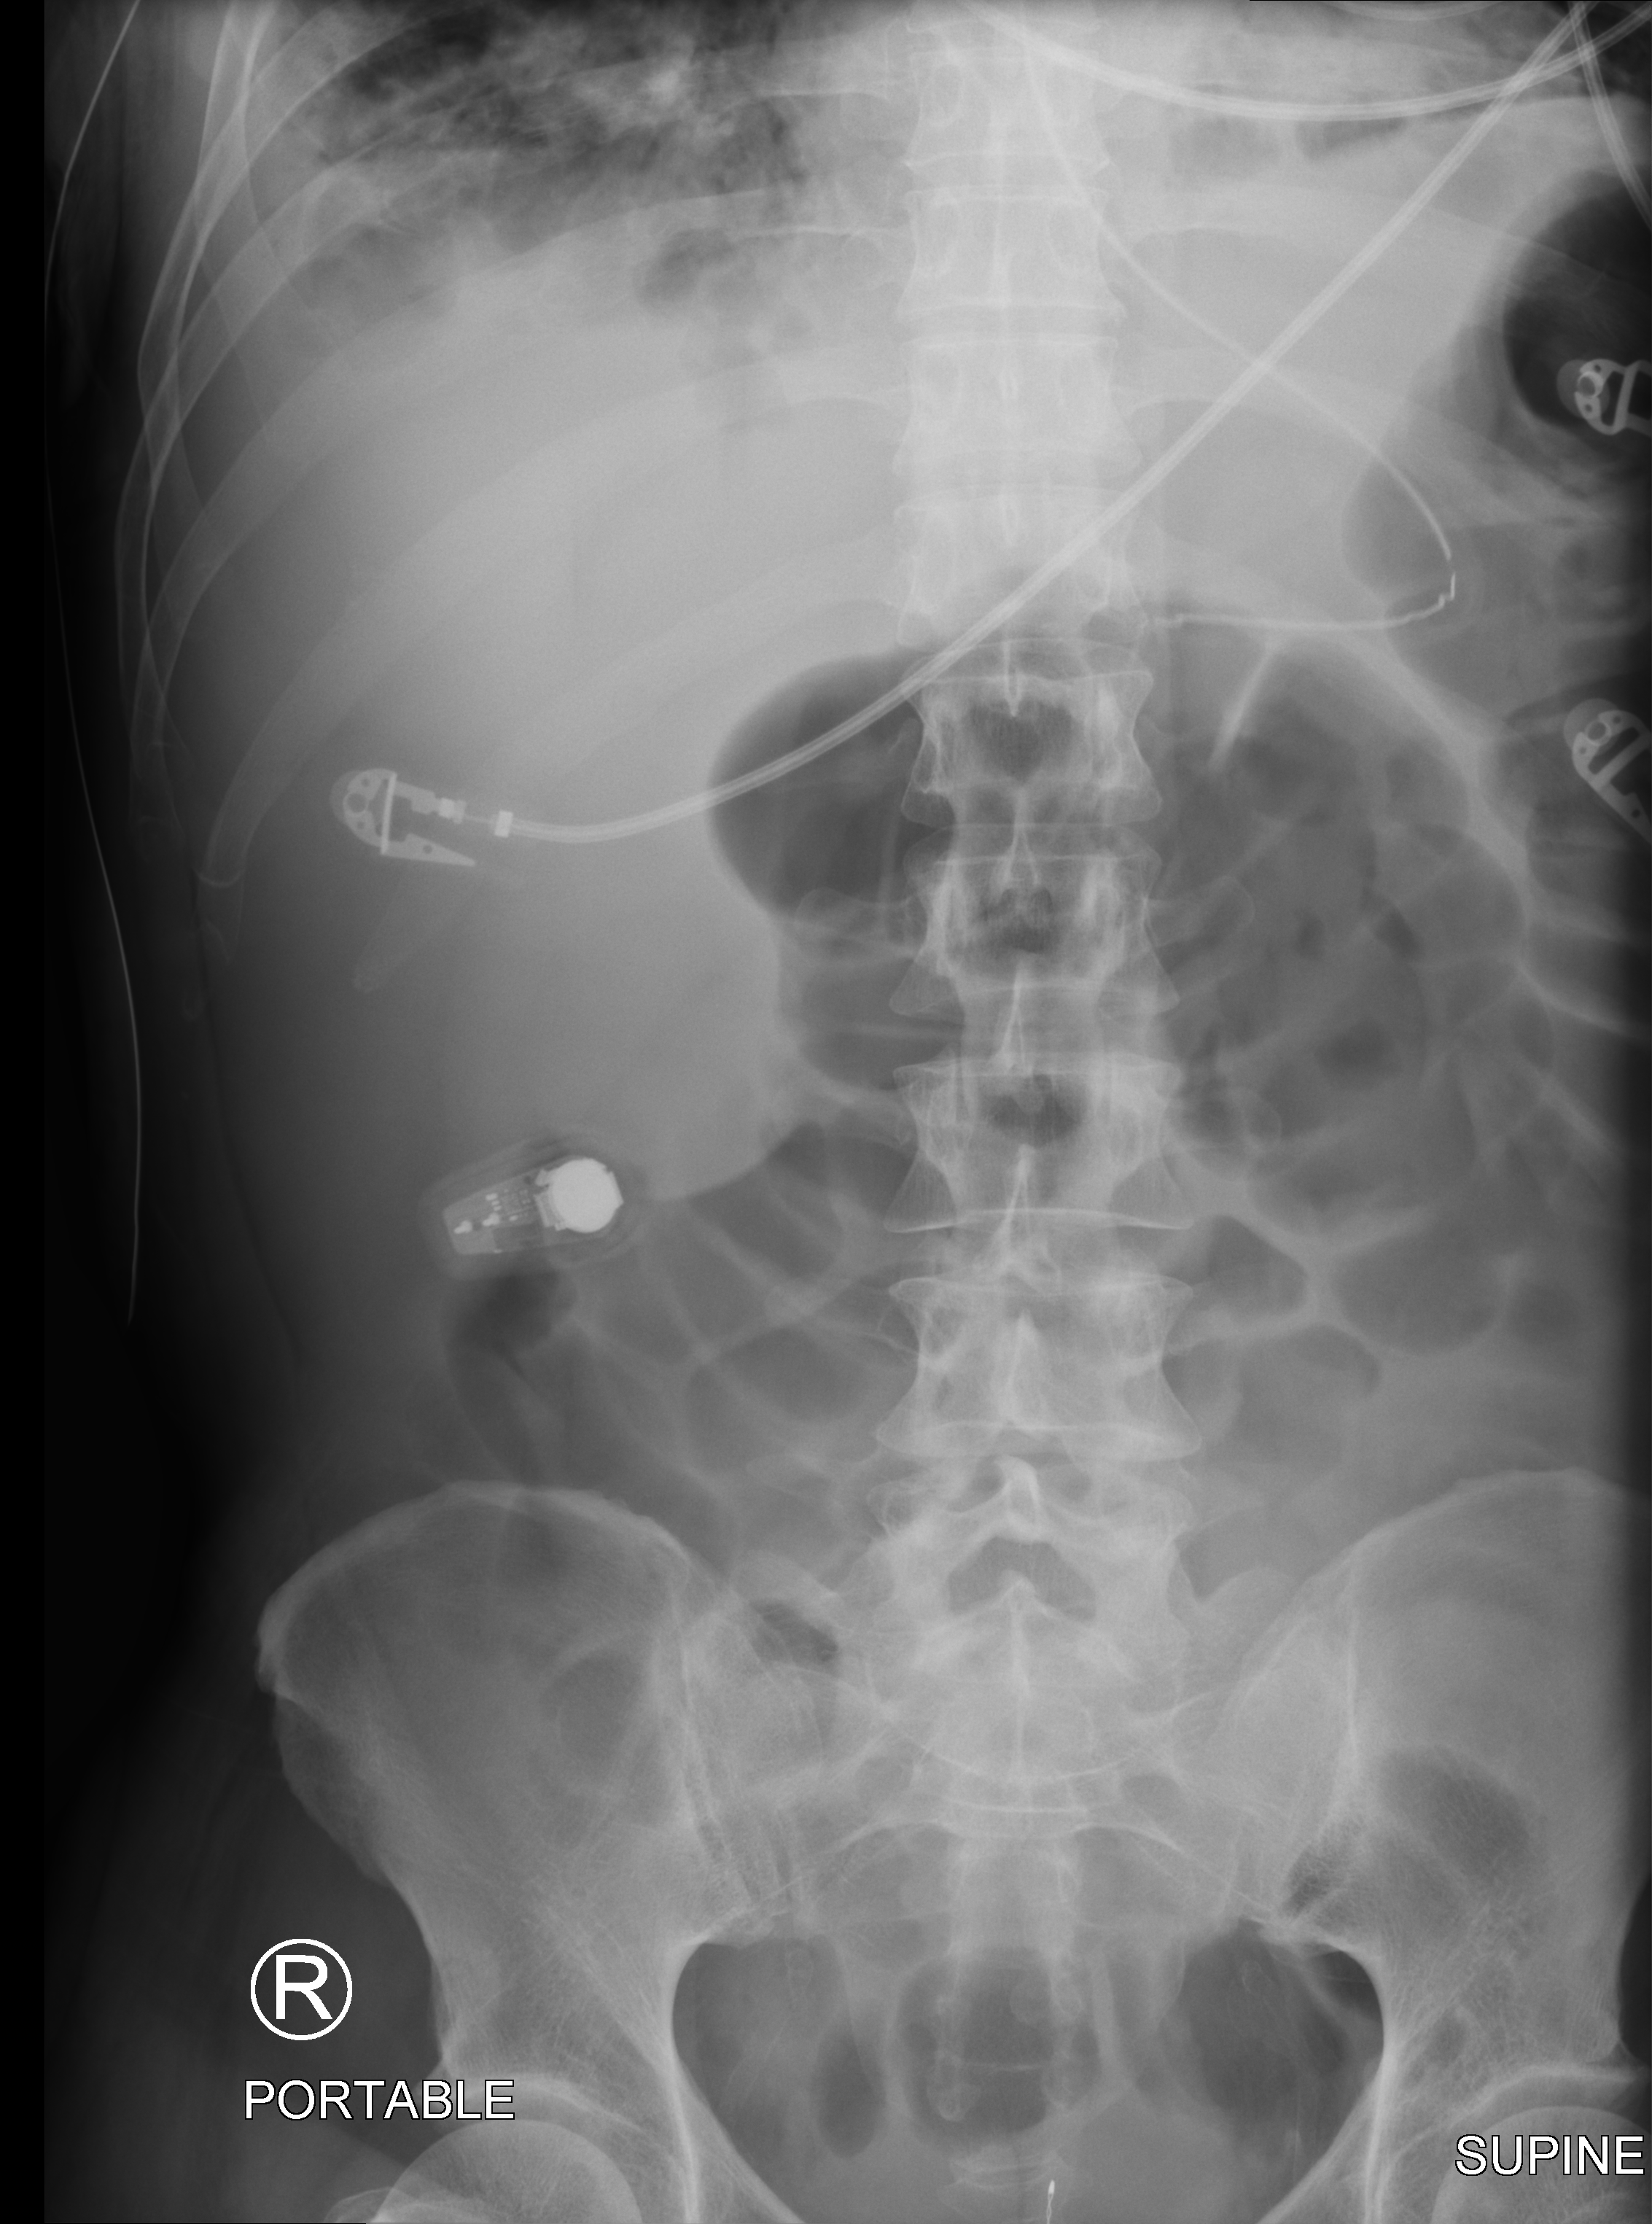
Portable abdomen radiograph. Patient hospitalised with COVID-19; male, aged 18–59 years.
Hospital-stay facts (about this admission, not read from this image; timing relative to this image not recorded):
- admitted to intensive care during this hospital stay: yes
- other chronic lung disease (admission record): no